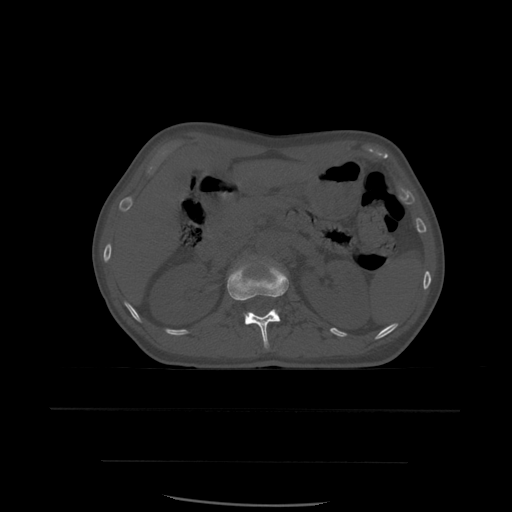
CT including the spine, one axial slice. Slice 246 of 574 in the series (ordered by position). Bone window (W 1800 / L 400 HU). 512 × 512 image matrix. Patient age 48 years. Case-level facts recorded for this patient, not image findings: primary cancer: lung; vertebrae with lytic lesions (as recorded): T11.
Annotated regions visible in this slice (semi-automatically segmented with operator editing):
- L1 vertebra: bounding box (x1, y1, x2, y2) in pixels: (227, 261, 289, 349)